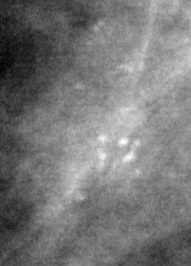
Region of interest cut from a scanned film mammogram (one marked finding), left breast, MLO view.
Calcifications, morphology pleomorphic, distribution clustered; BI-RADS assessment category 4; pathology result (as recorded, not read from the image): malignant.